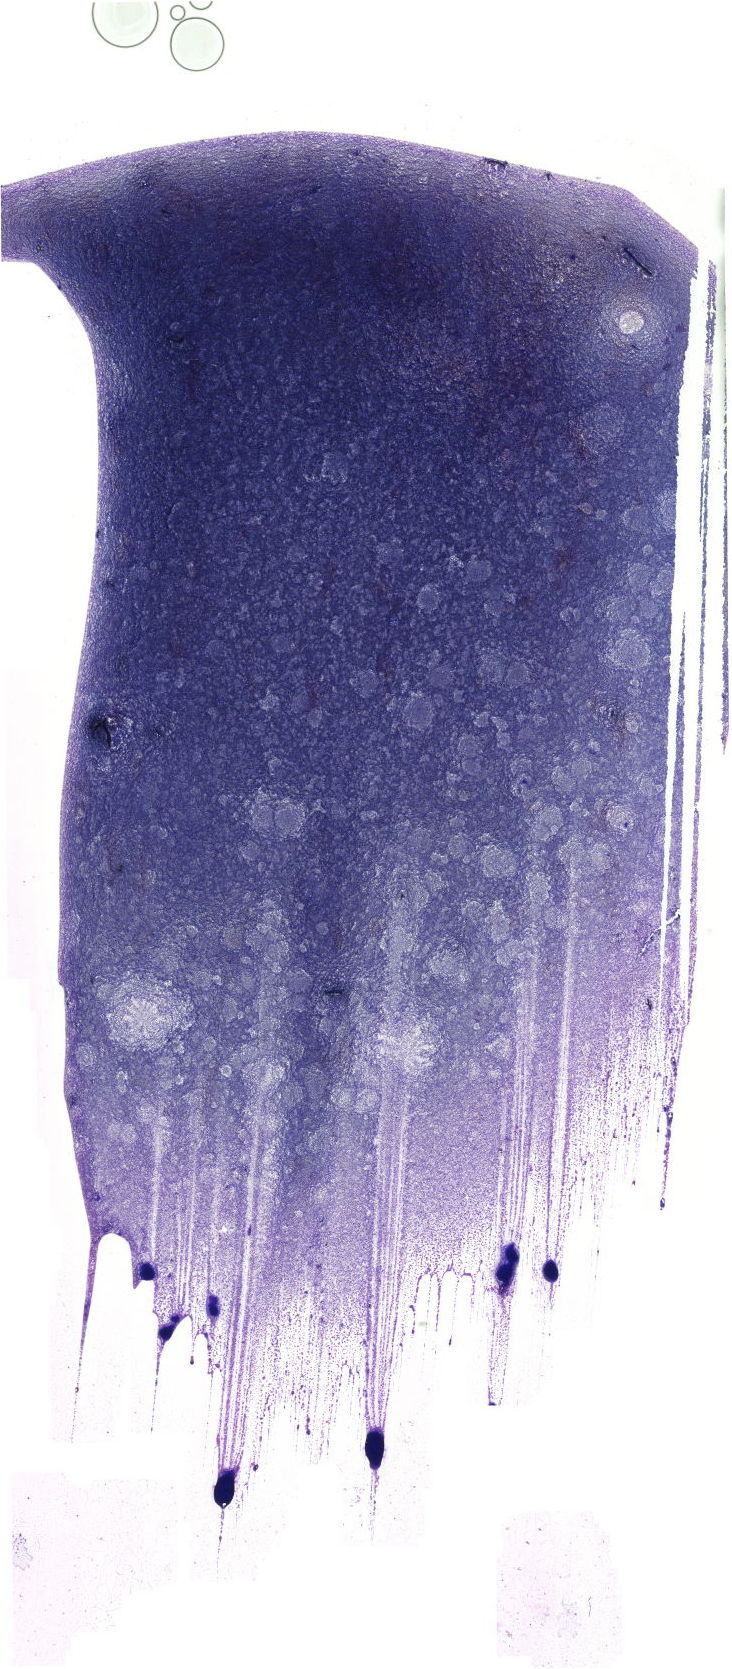
Bone marrow aspirate smear, May-Grünwald-Giemsa (MGG) stain, whole-slide image — a low-resolution overview of the entire scanned area, about 20.7 x 47.3 mm. Male patient.
• diagnosis: Chronic Phase Chronic Myeloid Leukemia, BCR-ABL1 Positive